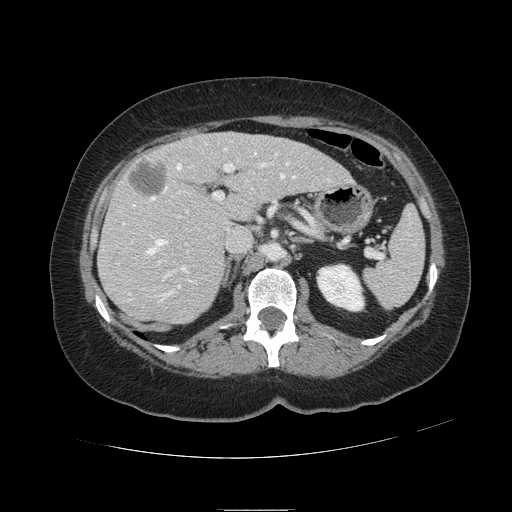
Contrast-enhanced abdominal CT, one axial slice. Slice 63 of 121 in the series (ordered by position). Intravenous contrast given. Soft-tissue window (W 400 / L 40 HU). 2.5 mm slice thickness. 512 × 512 image matrix, field of view 400 × 400 mm. Female patient, age 52 years. From the clinical record (not read from this slice): diagnosis: colorectal cancer liver metastases, imaged before liver resection; multiple liver metastases: yes; largest metastasis: 6.3 cm.
Outlined on this slice (manually delineated by an expert):
- hepatic veins: bounding box [x1, y1, x2, y2] px = [133, 148, 330, 302]
- liver: [100, 133, 352, 324]
- planned liver remnant (the part of the liver to remain after resection): [167, 133, 352, 221]
- portal vein (with intrahepatic branches): [123, 153, 278, 278]
- liver metastasis: [129, 163, 167, 196]